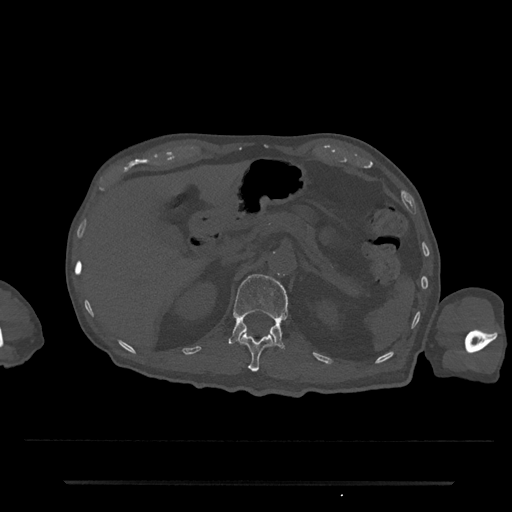
CT including the spine, one axial slice. Position 160 of 797 along the scan axis. Reconstruction kernel Br40s/3. 120 kVp. Bone window (W 1800 / L 400 HU). 0.5 mm slice thickness. 512 × 512 image matrix, field of view 427 × 427 mm. Male patient, age 74 years. From the clinical record (not read from this slice): primary cancer: prostate.
Outlined on this slice (semi-automatic segmentation, software-assisted and operator-edited):
- L1 vertebra: bounding box [x1, y1, x2, y2] px = [228, 274, 288, 349]
- T12 vertebra: [240, 333, 273, 372]